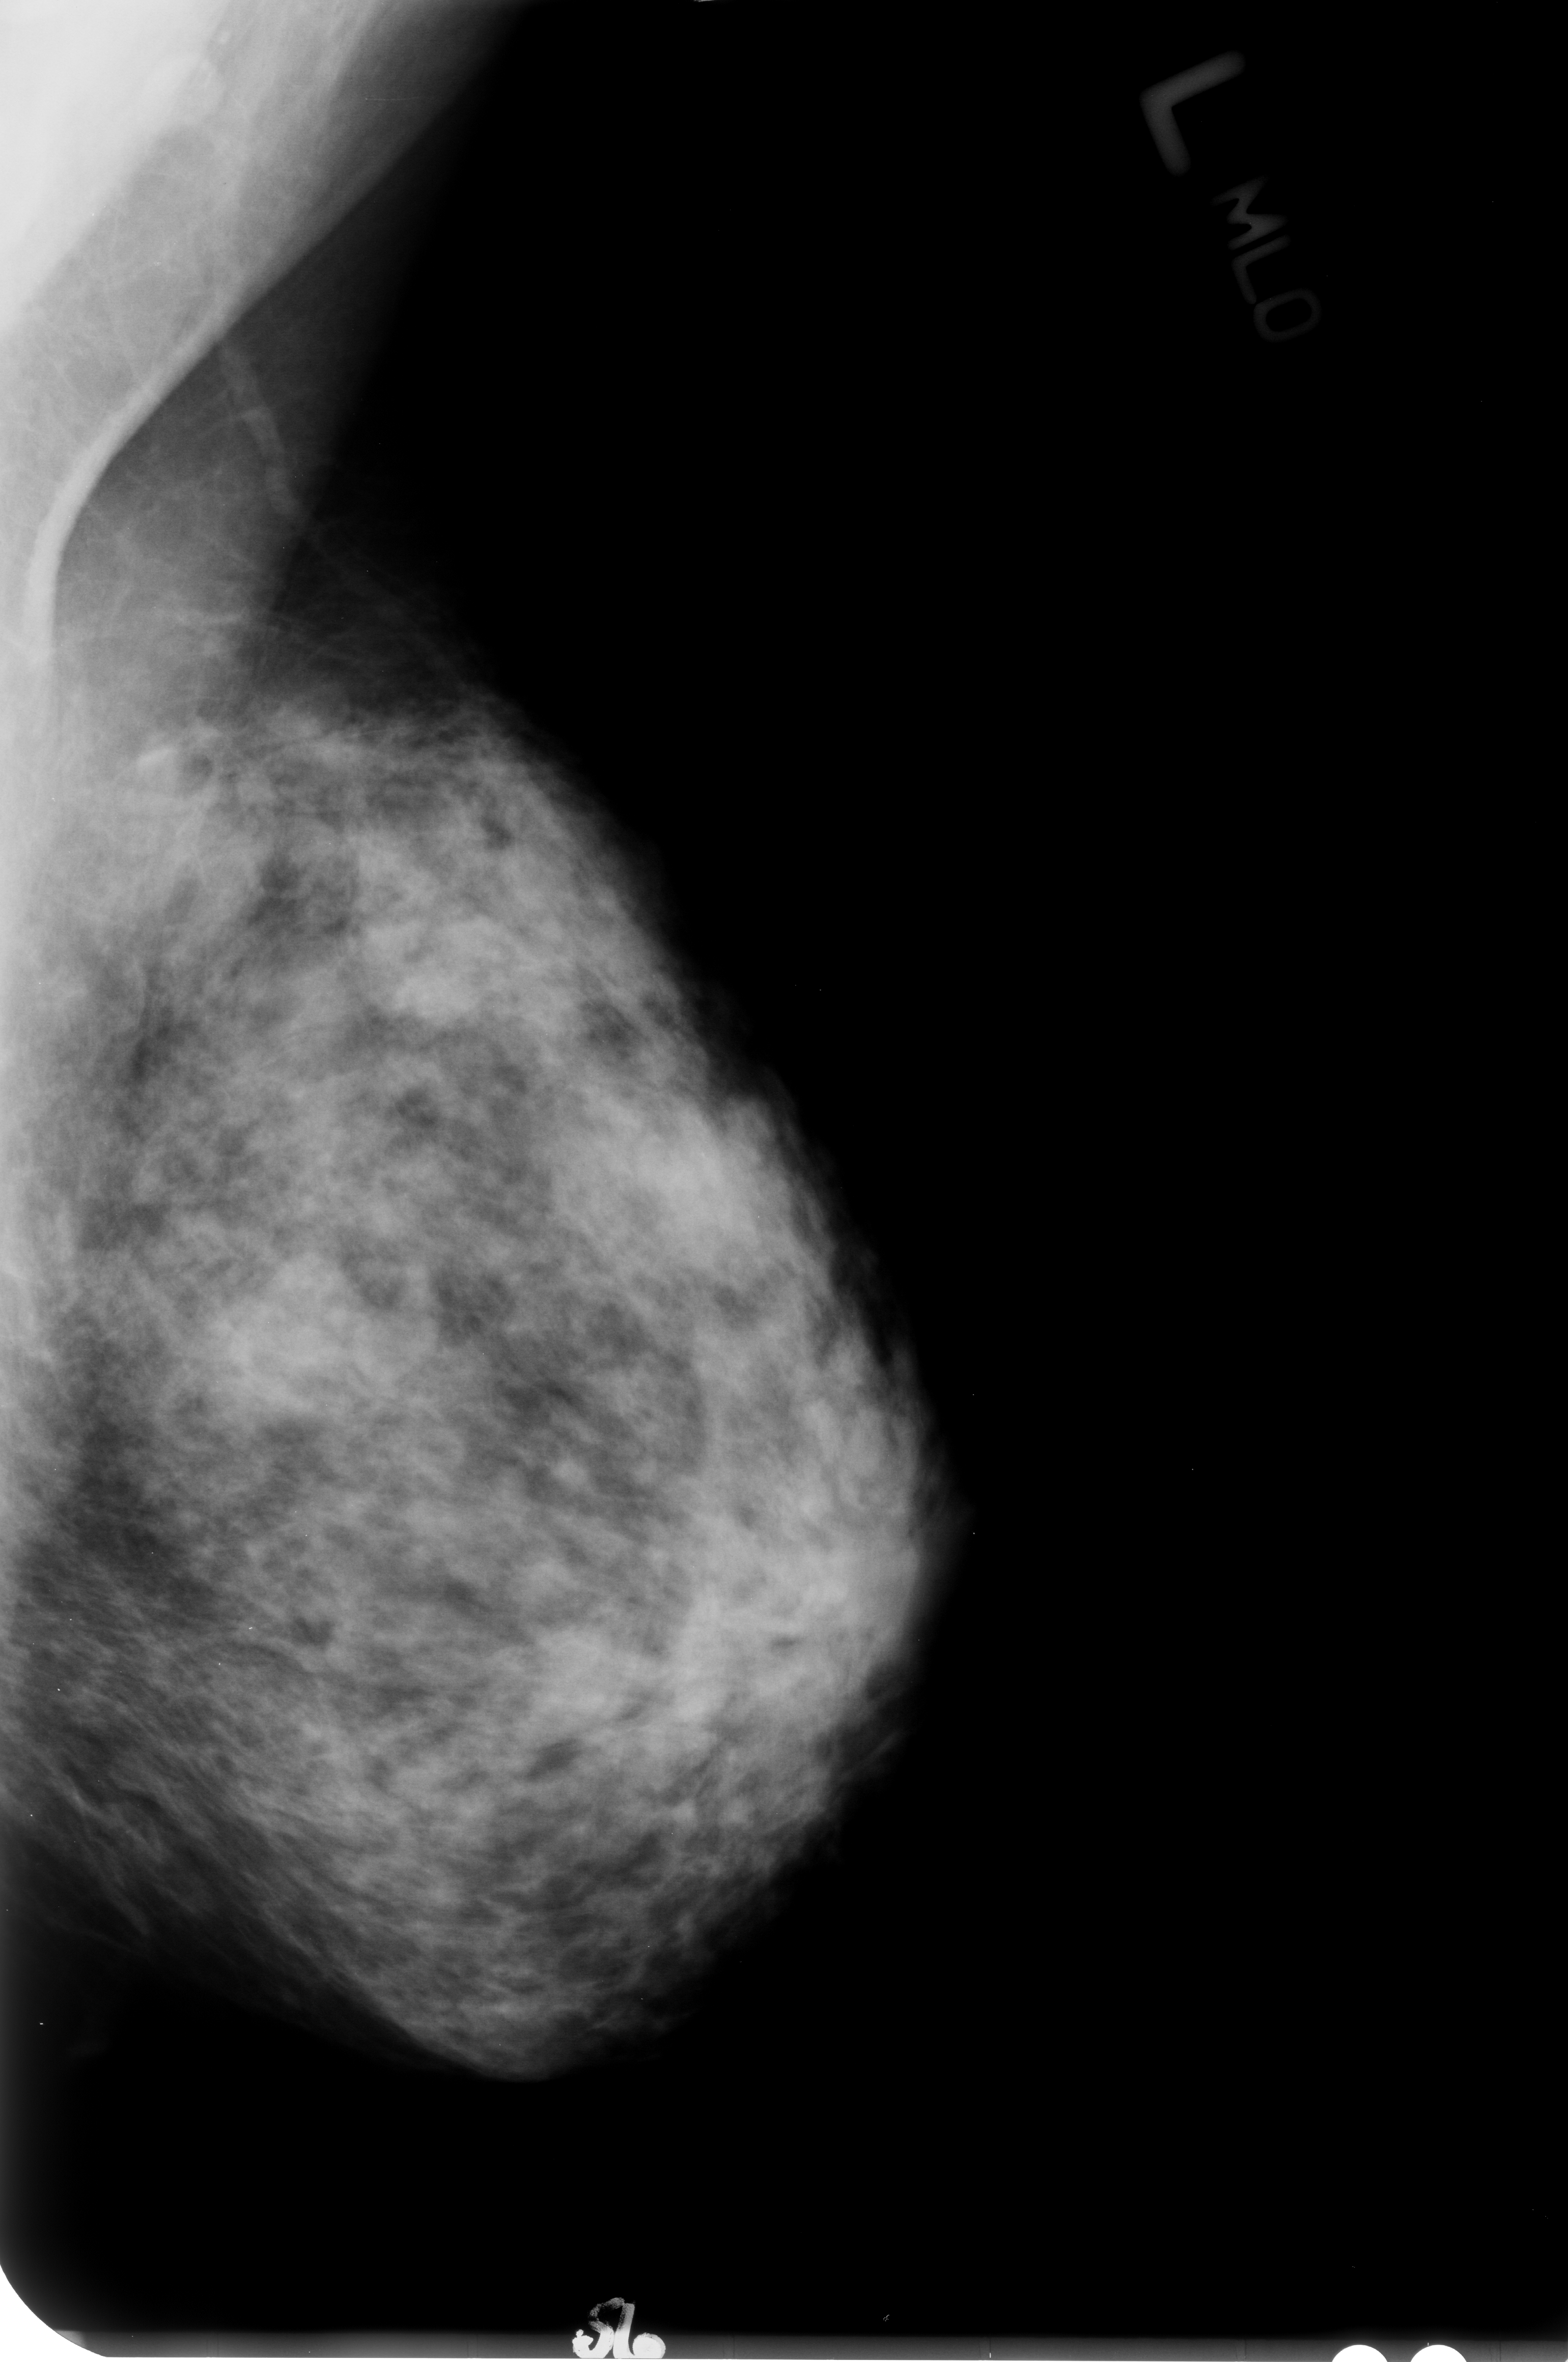
Mammogram (digitized film). Left breast. MLO view. BI-RADS breast density category 3 (scale 1–4). 1568 × 2362 image matrix.
Expert-marked regions of interest on this image (one box per marked abnormality):
- mass, shape oval, margins circumscribed / obscured; BI-RADS assessment category 4; subtlety rating 2 on a 1 (subtle) to 5 (obvious) scale; pathology result (as recorded, not read from the image): benign: bounding box [x1, y1, x2, y2] px = [224, 1260, 389, 1432]